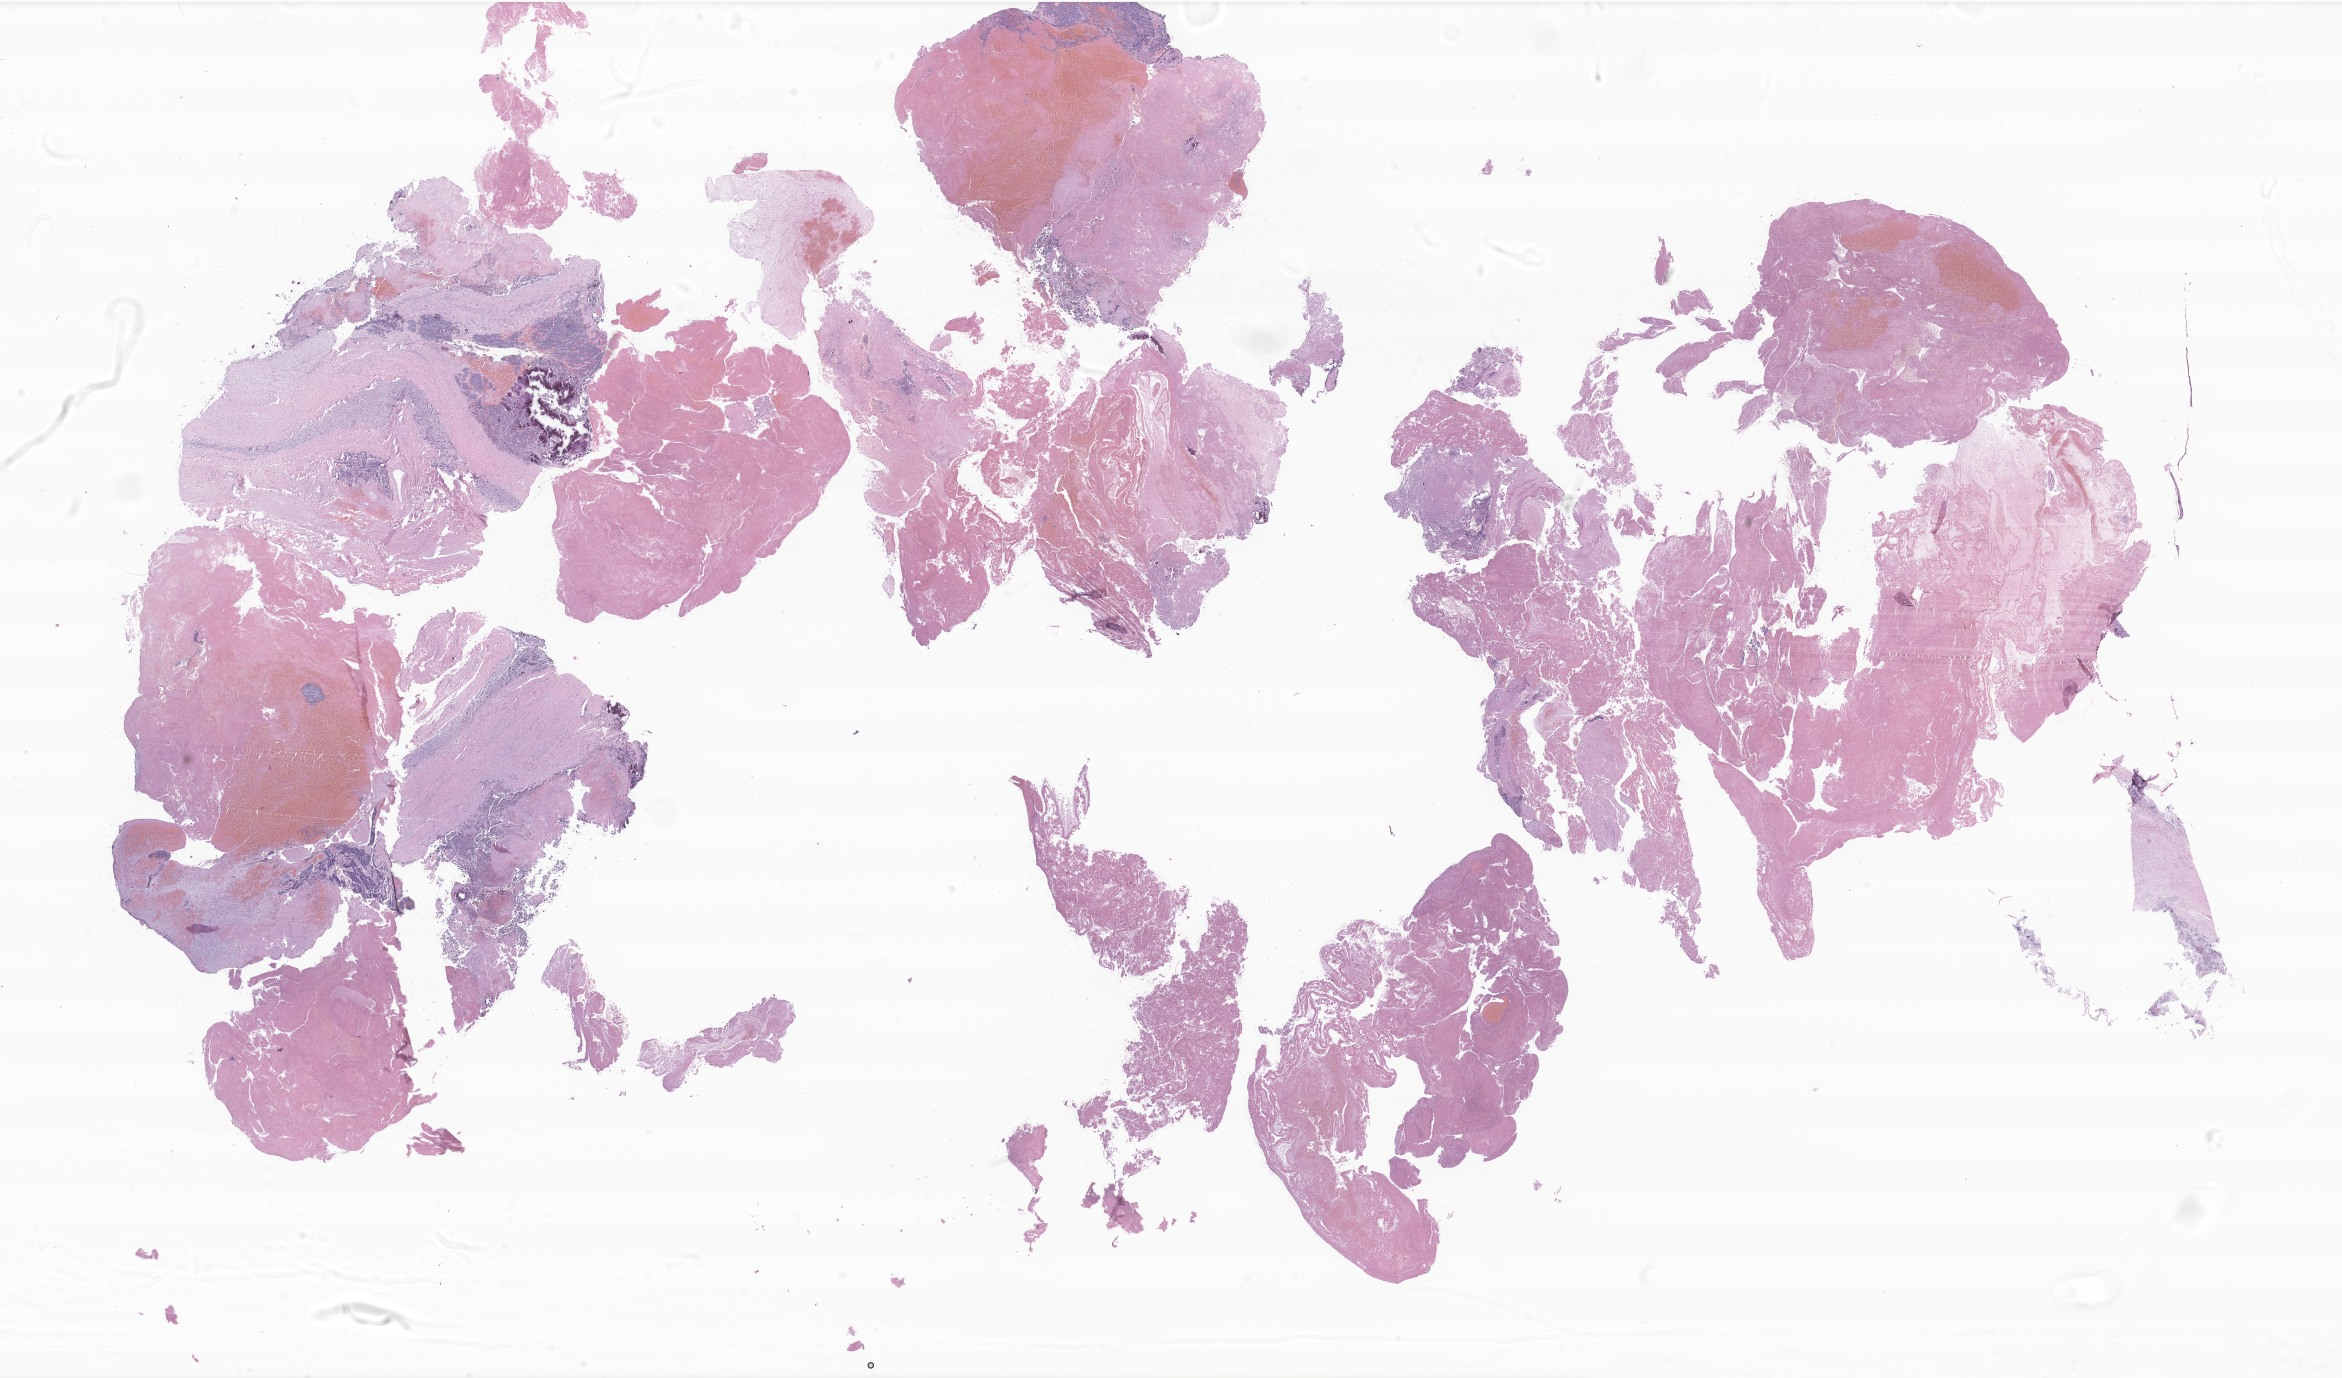
Digitized haematoxylin and eosin-stained section of tumor tissue from the adrenal gland — a low-resolution overview of the entire scanned area, about 39.5 x 23.2 mm. Formalin-fixed paraffin-embedded section. Female patient, age 374 days.
• diagnosis: Neuroblastoma, NOS